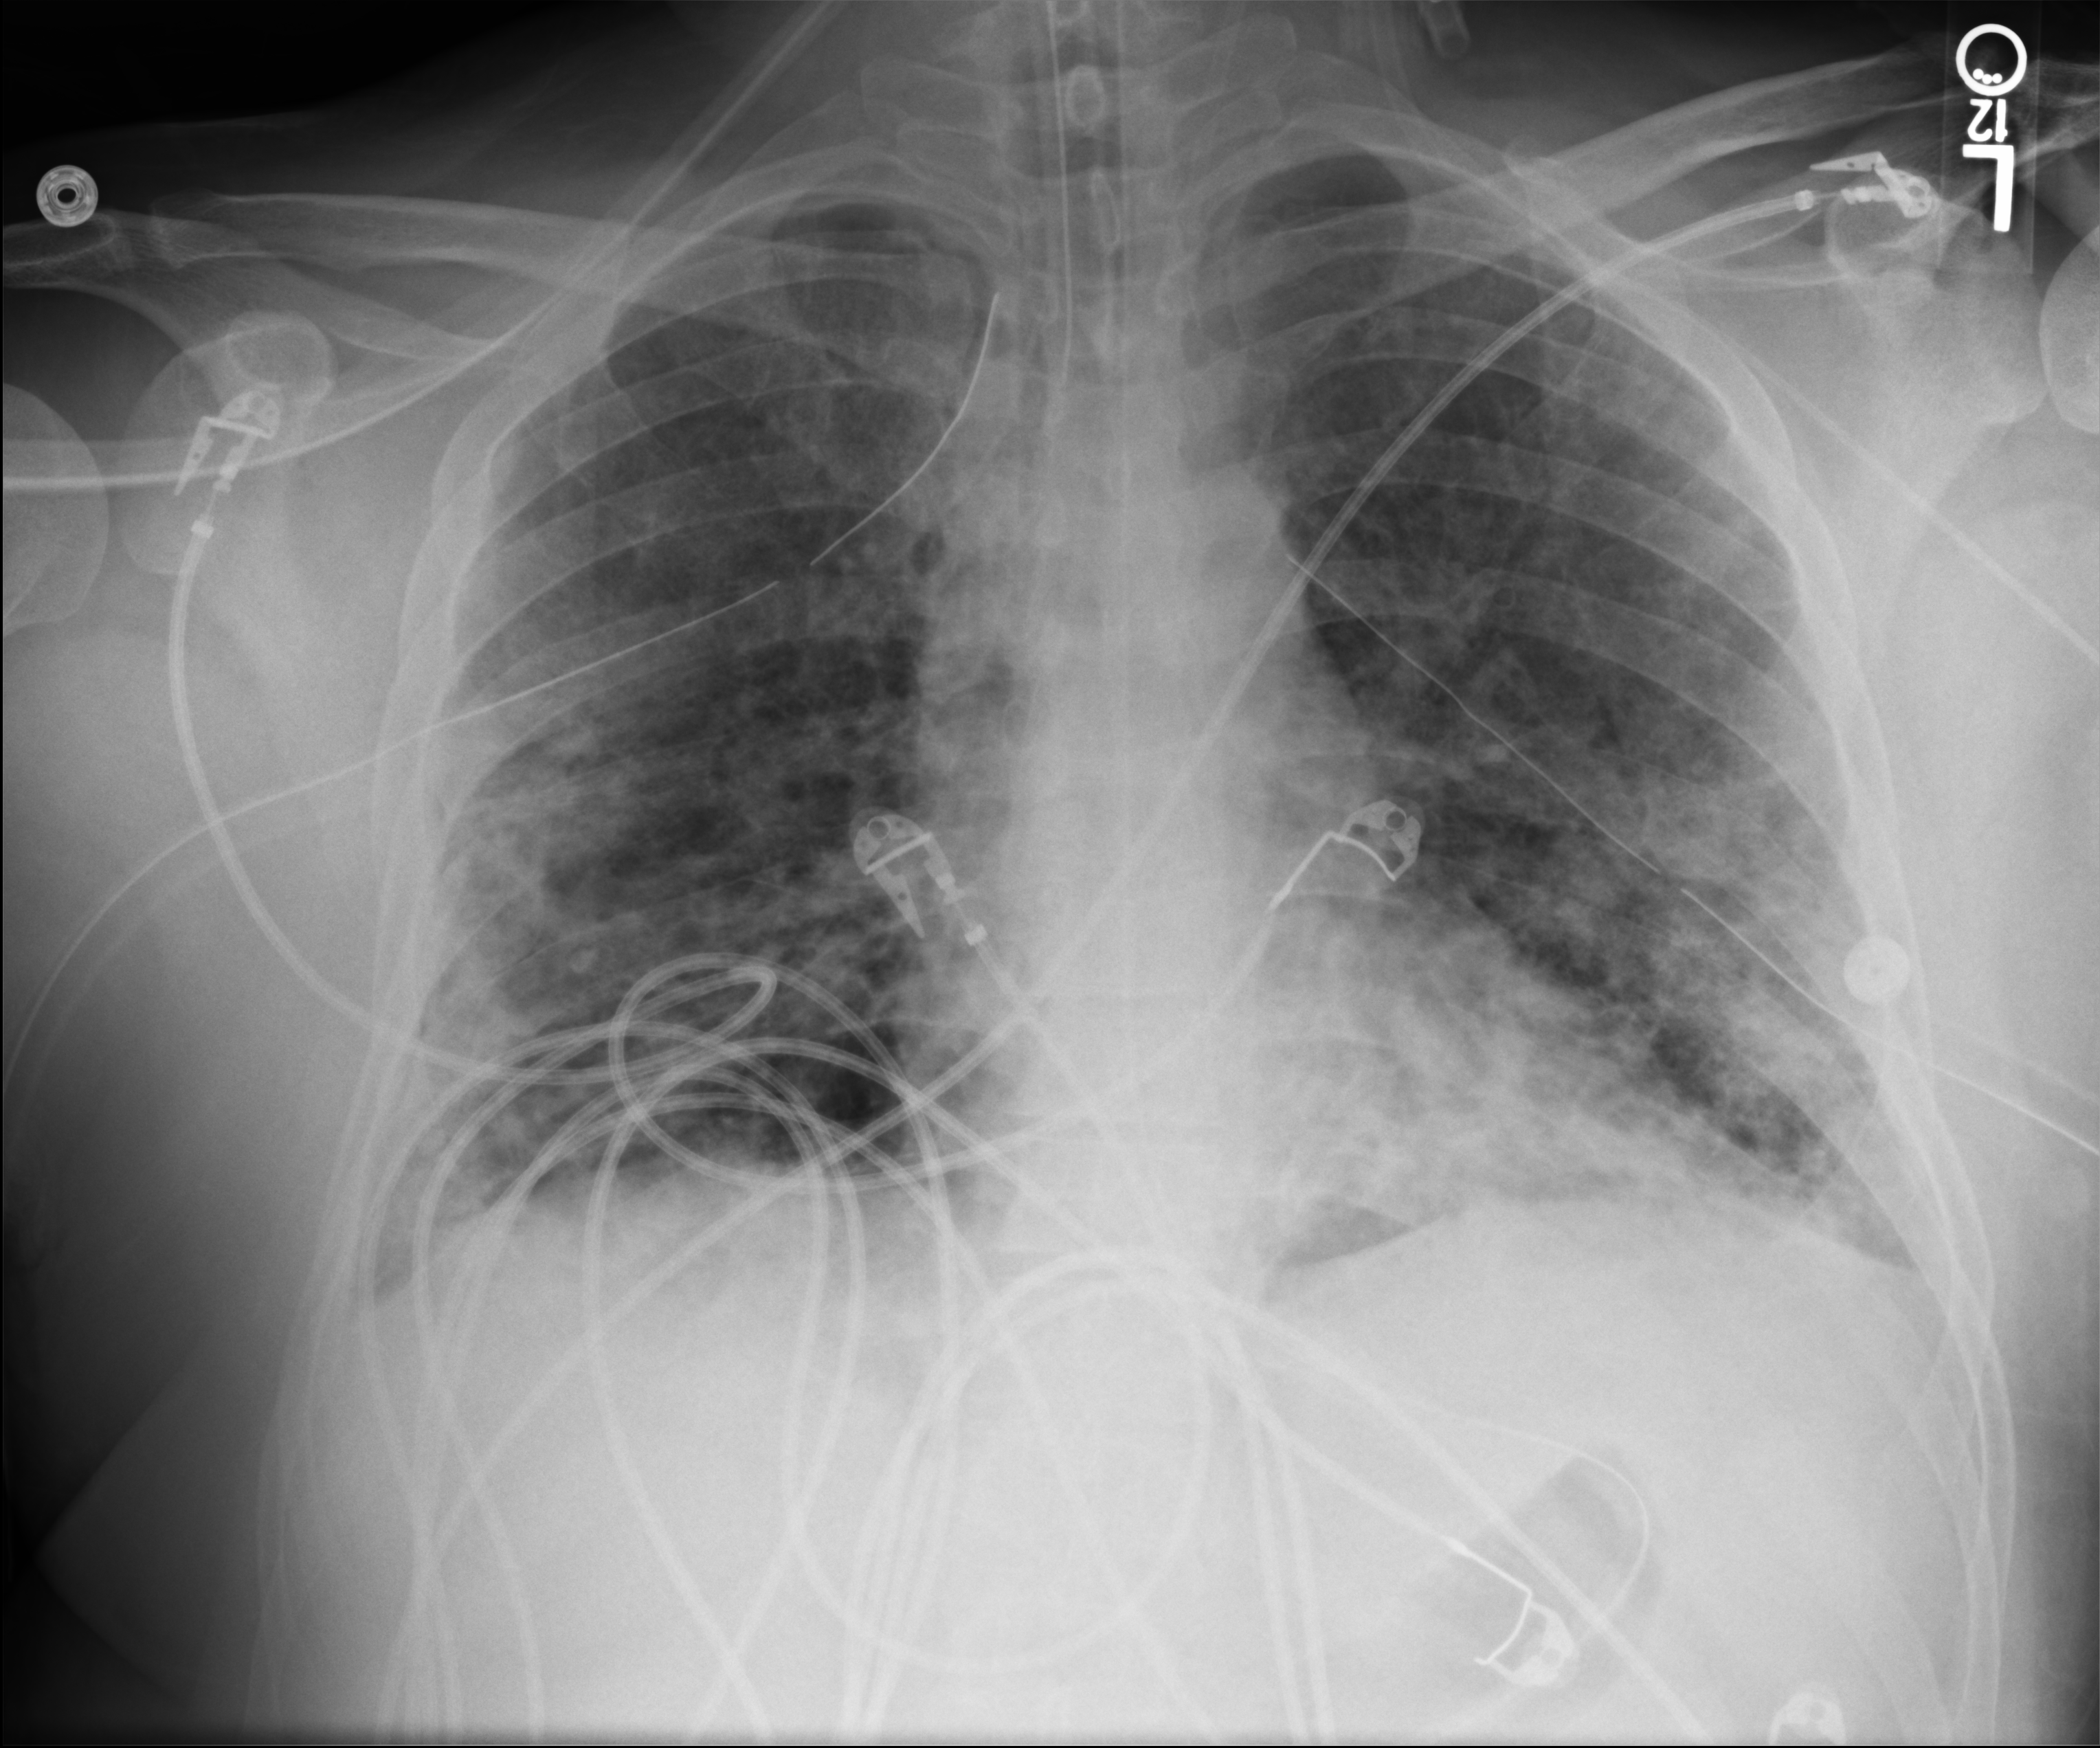
Portable chest radiograph, anteroposterior (AP) projection. Male patient hospitalised with COVID-19, age 18–59 years.
Admission-level facts for this patient (not findings on this image; timing relative to this image not recorded):
- mechanically ventilated during this hospital stay: yes